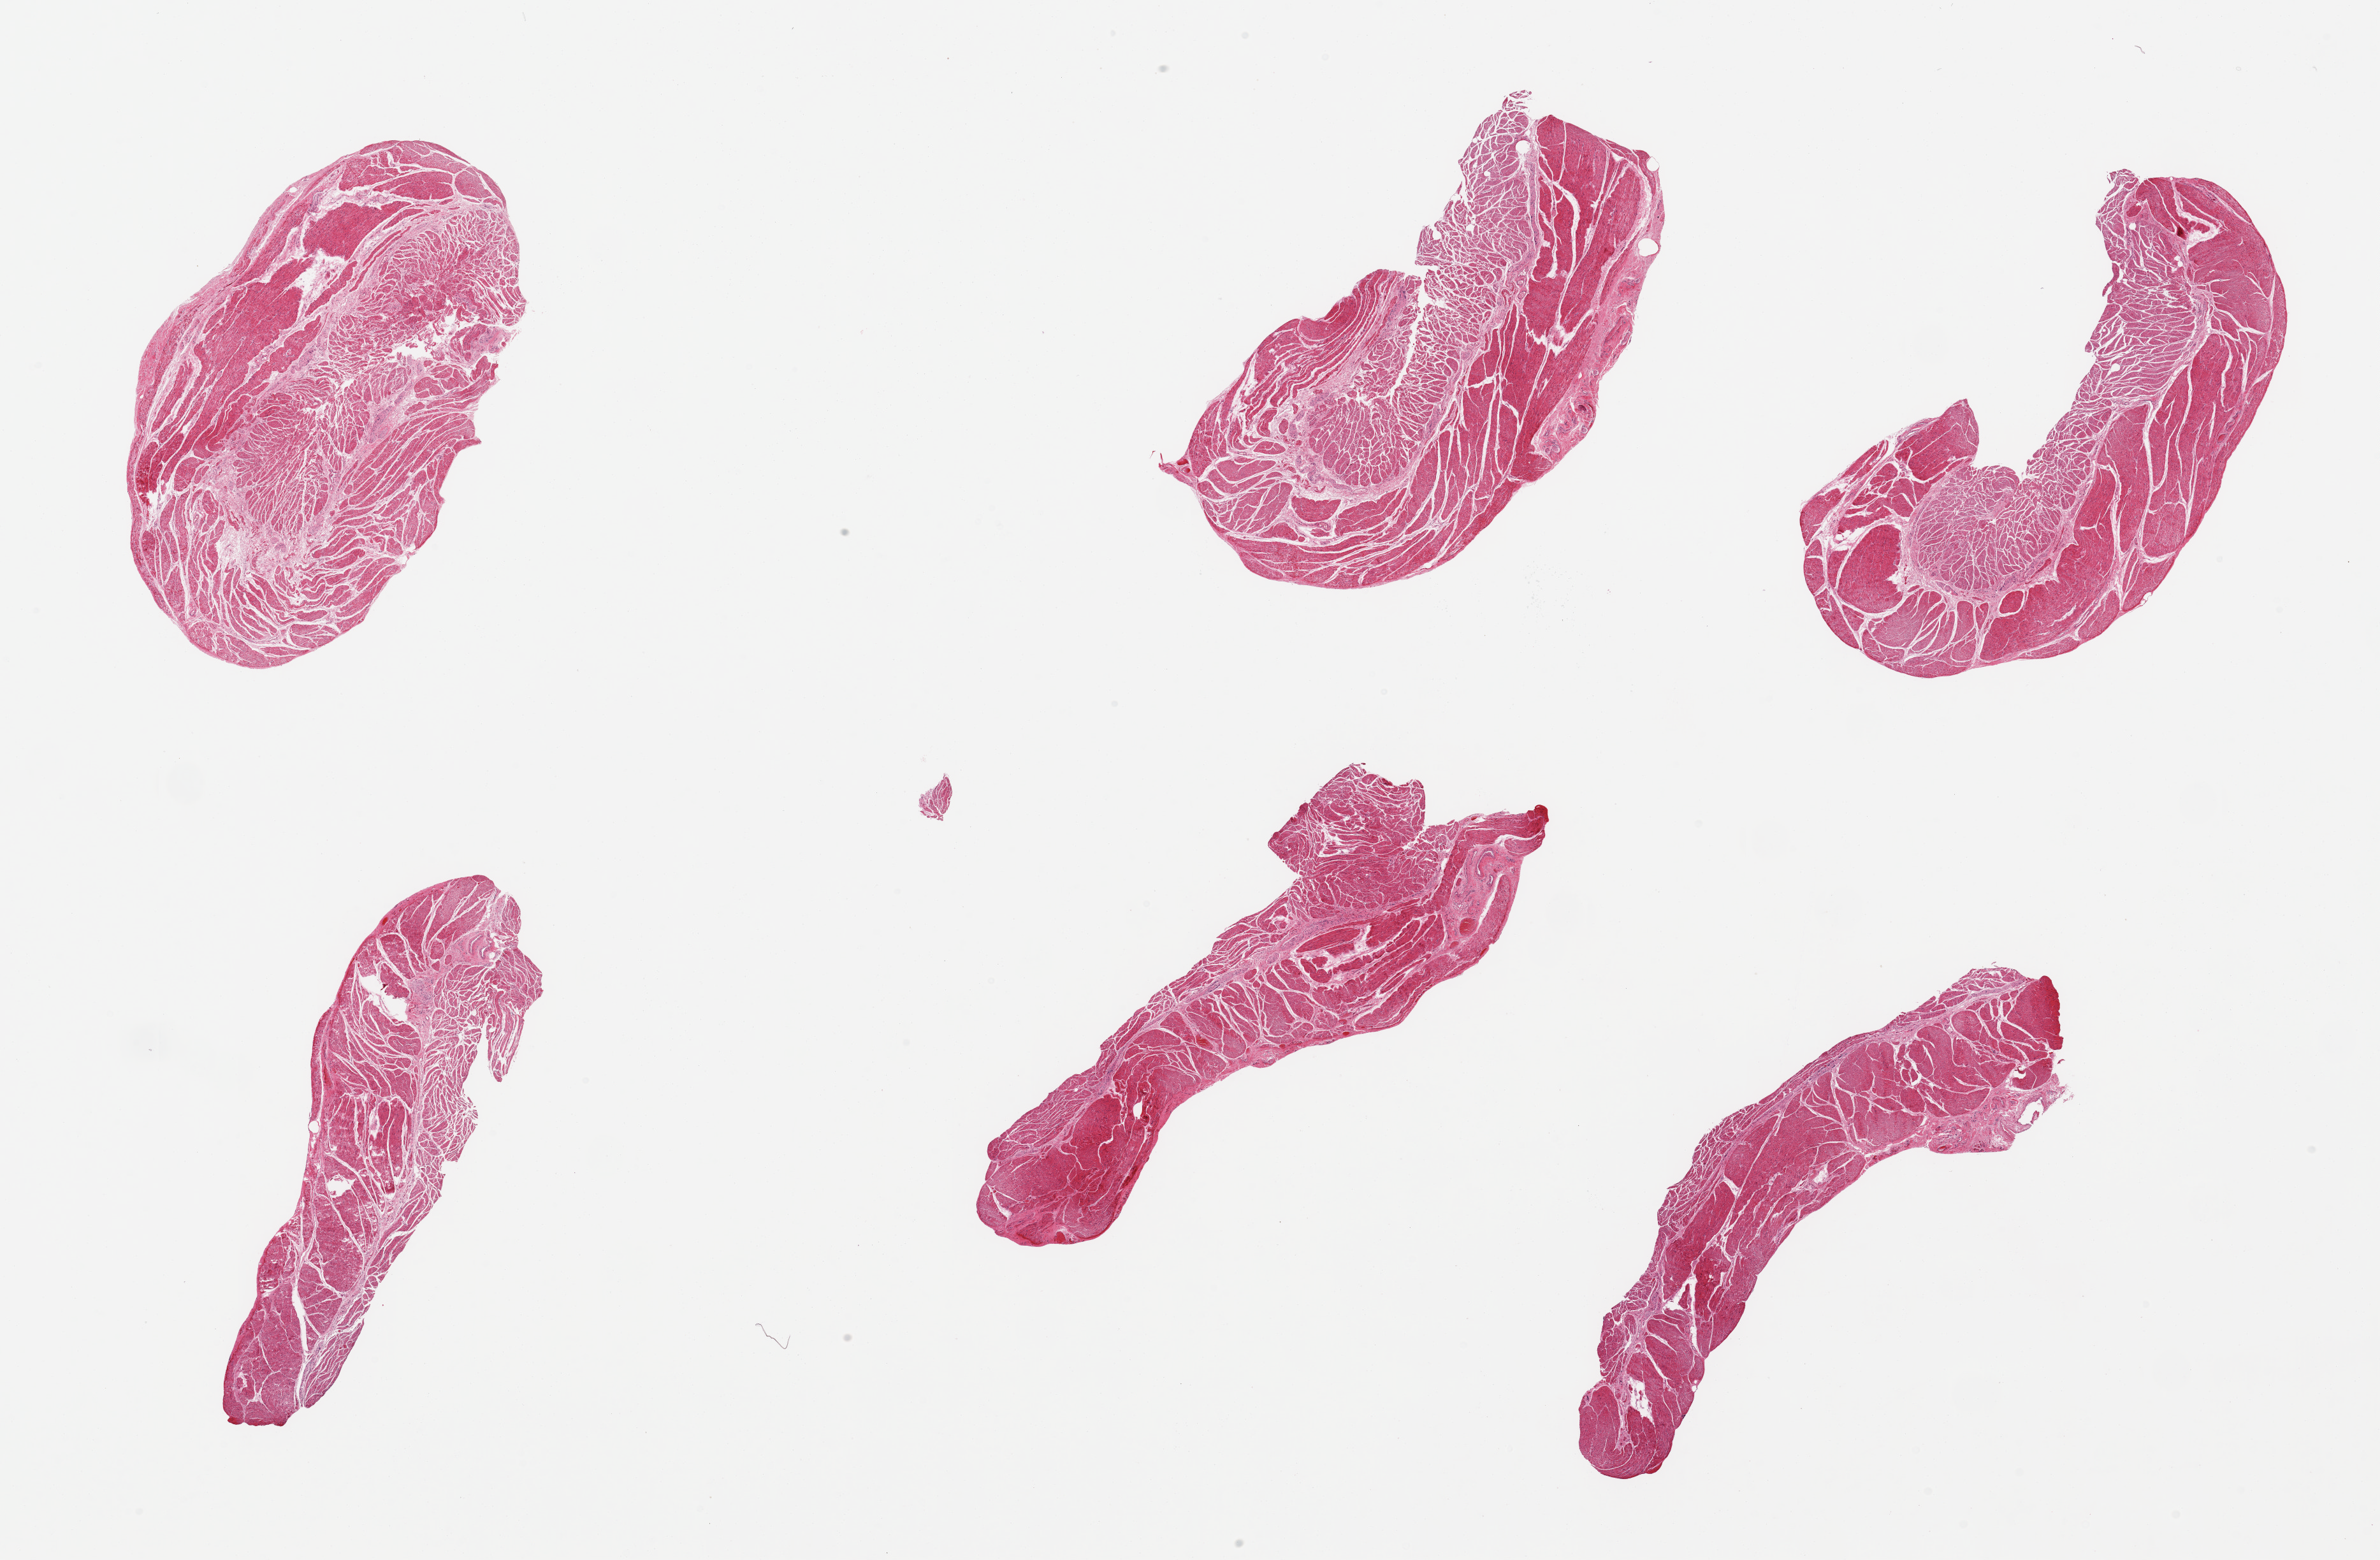
Haematoxylin and eosin whole-slide image — a low-resolution overview of the entire scanned area, about 29.5 x 19.4 mm. PAXgene-fixed paraffin-embedded (PFPE) section. Target tissue: esophageal muscle. Tissue donor sample. Male donor.
Pathologist's review note for this sample: 6 pieces, confirmed target muscularis.